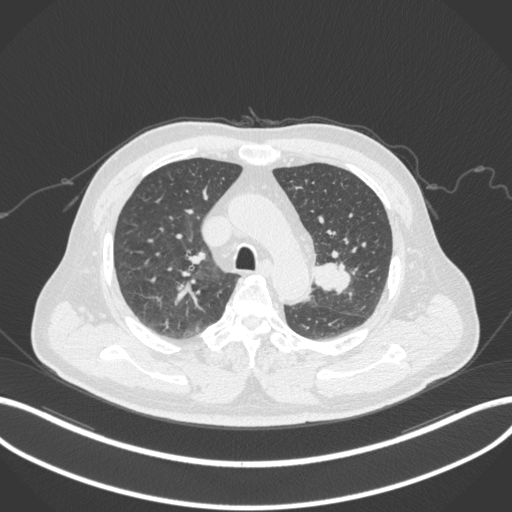
Chest CT, one axial slice; position 213 of 286 along the scan axis; 120 kVp; lung window (W 1500 / L -600 HU); 1 mm slice thickness; 512 × 512 image matrix, field of view 400 × 400 mm. Male patient, age 67 years. From the clinical record (not read from this slice): clinical TNM (as recorded): T2a N1 M0.
Annotated regions visible in this slice (rectangle marked by the reading radiologist):
- lung tumour (recorded histology: adenocarcinoma): box from (x=314, y=259) to (x=351, y=296) px